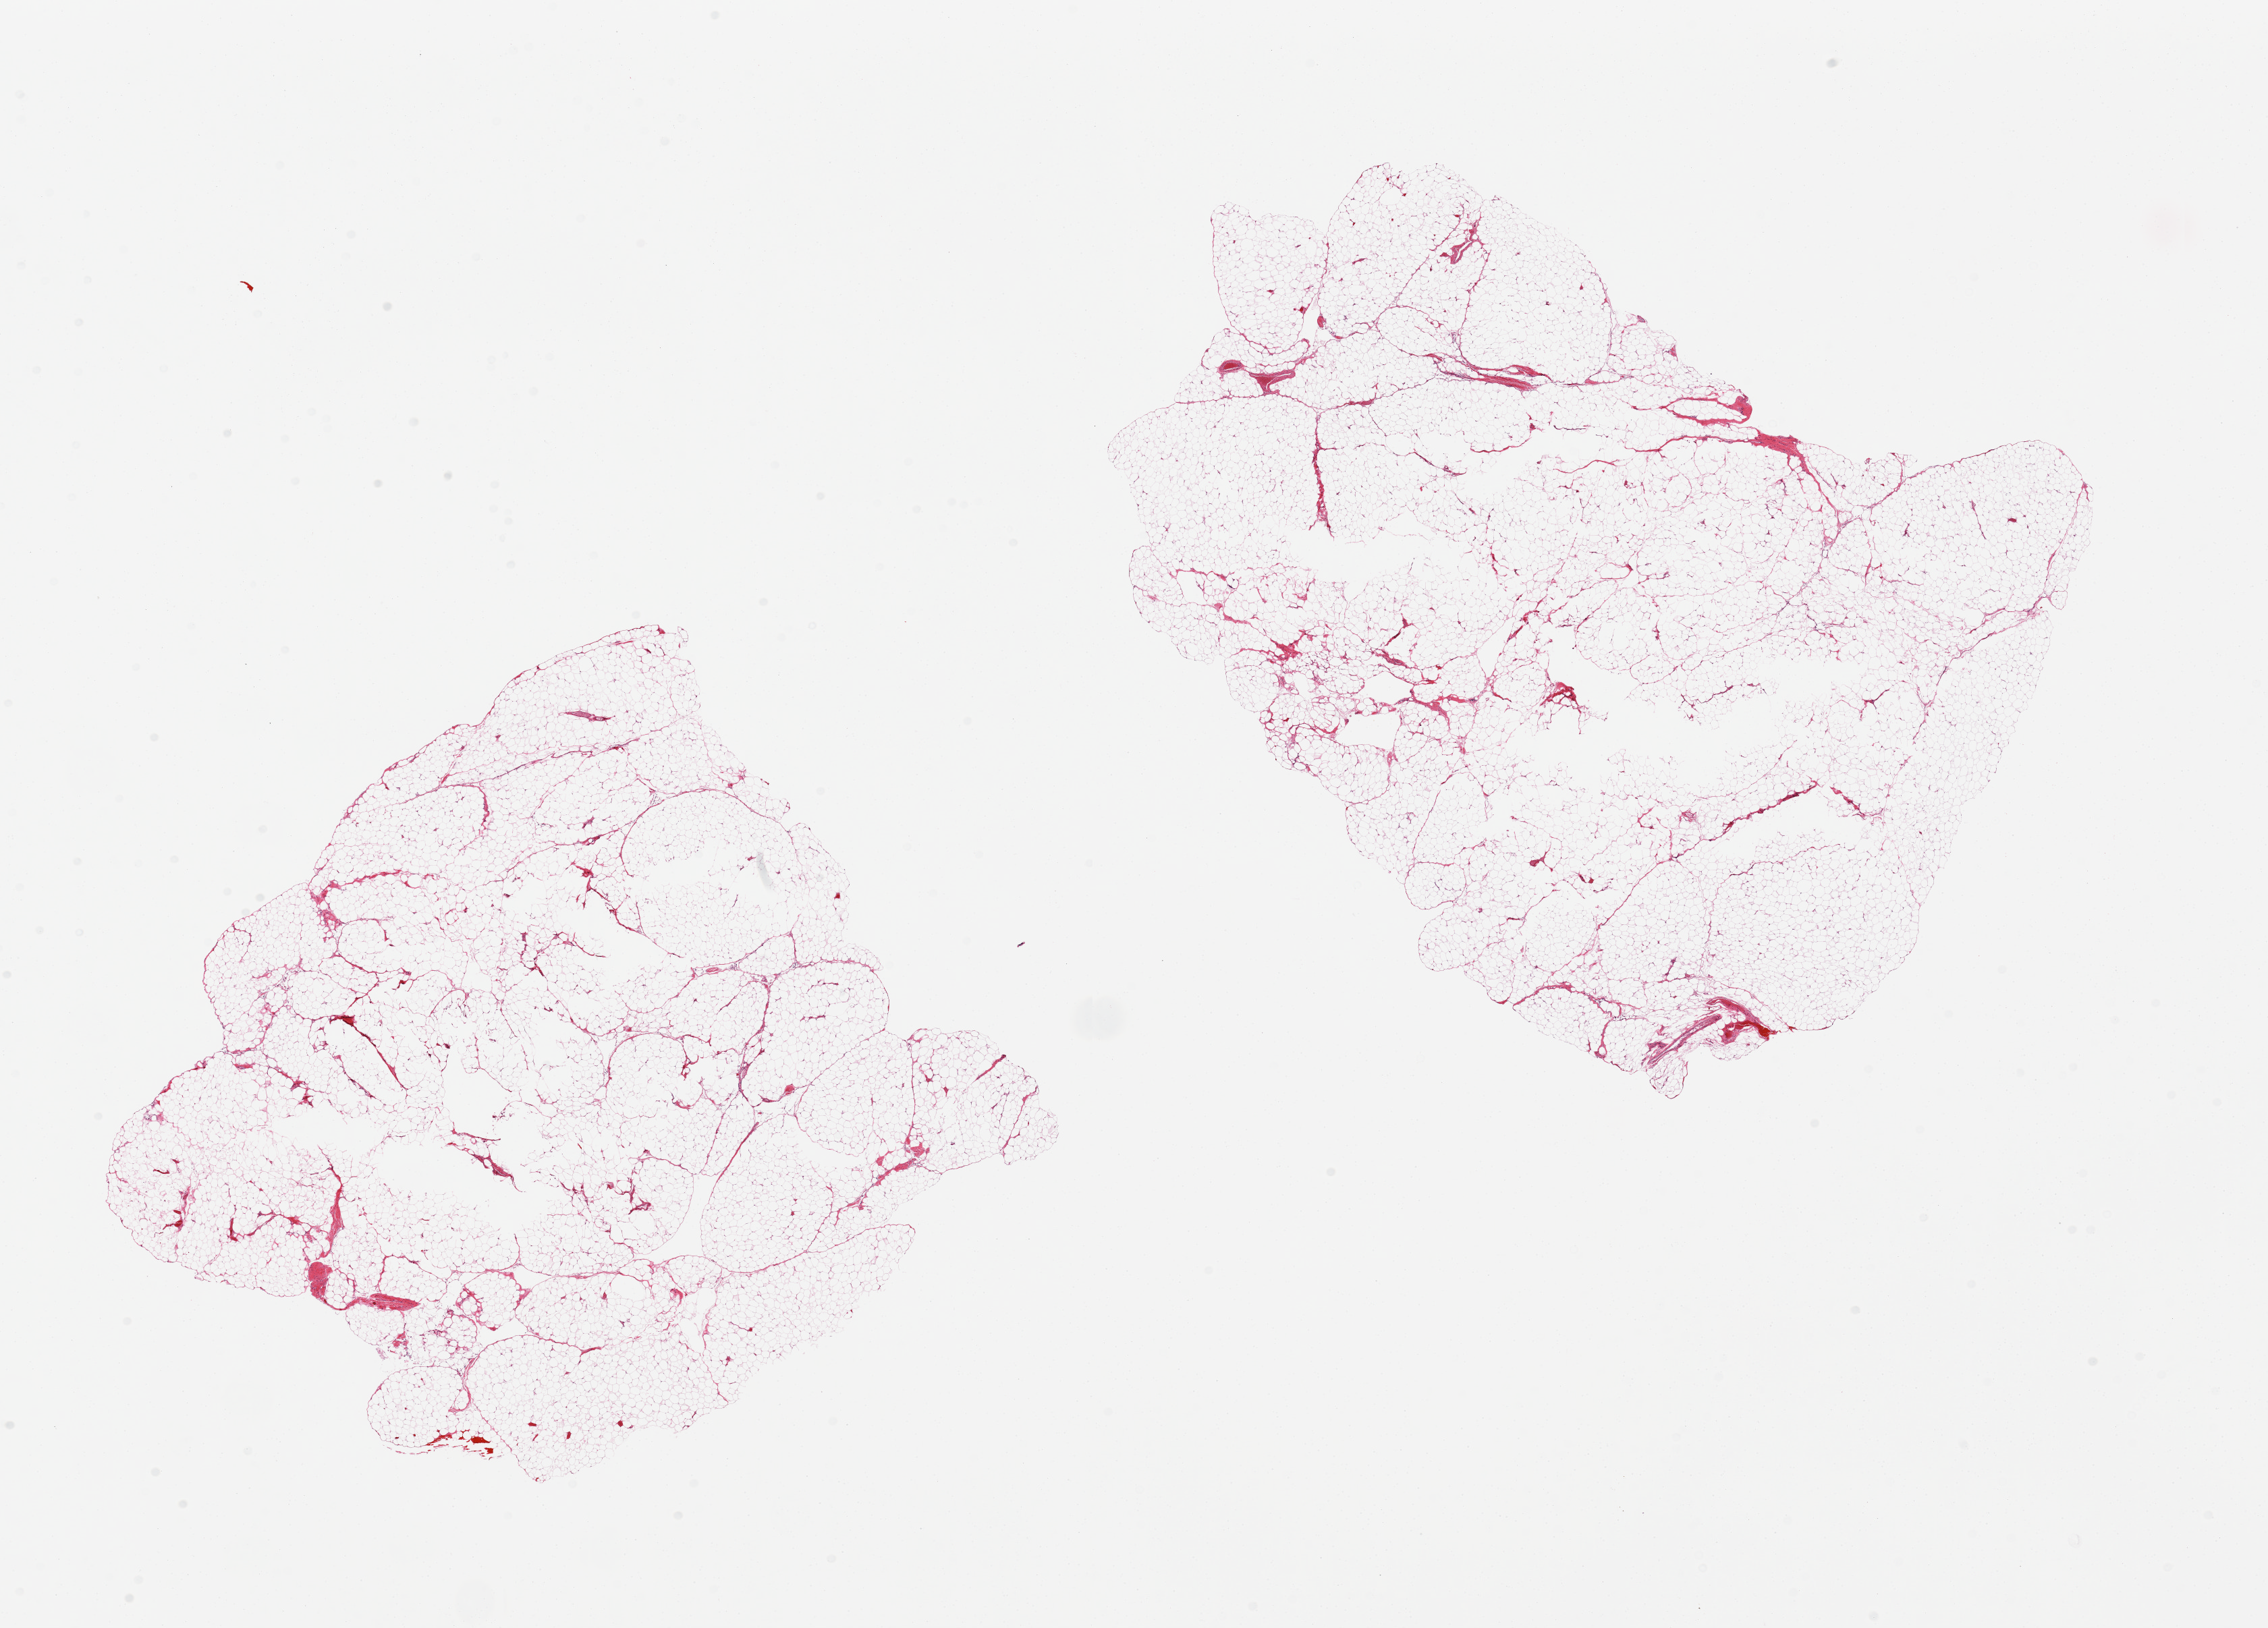
Whole-slide image, hematoxylin and eosin (H&E) stain — a low-resolution overview of the entire scanned area, about 26.6 x 19.1 mm (from a 20x scan); PAXgene-fixed, paraffin-embedded tissue; target tissue: omentum; tissue donor sample. Donor sex: male.
* pathologist's review note for this sample: 2 pieces; scattered central holes